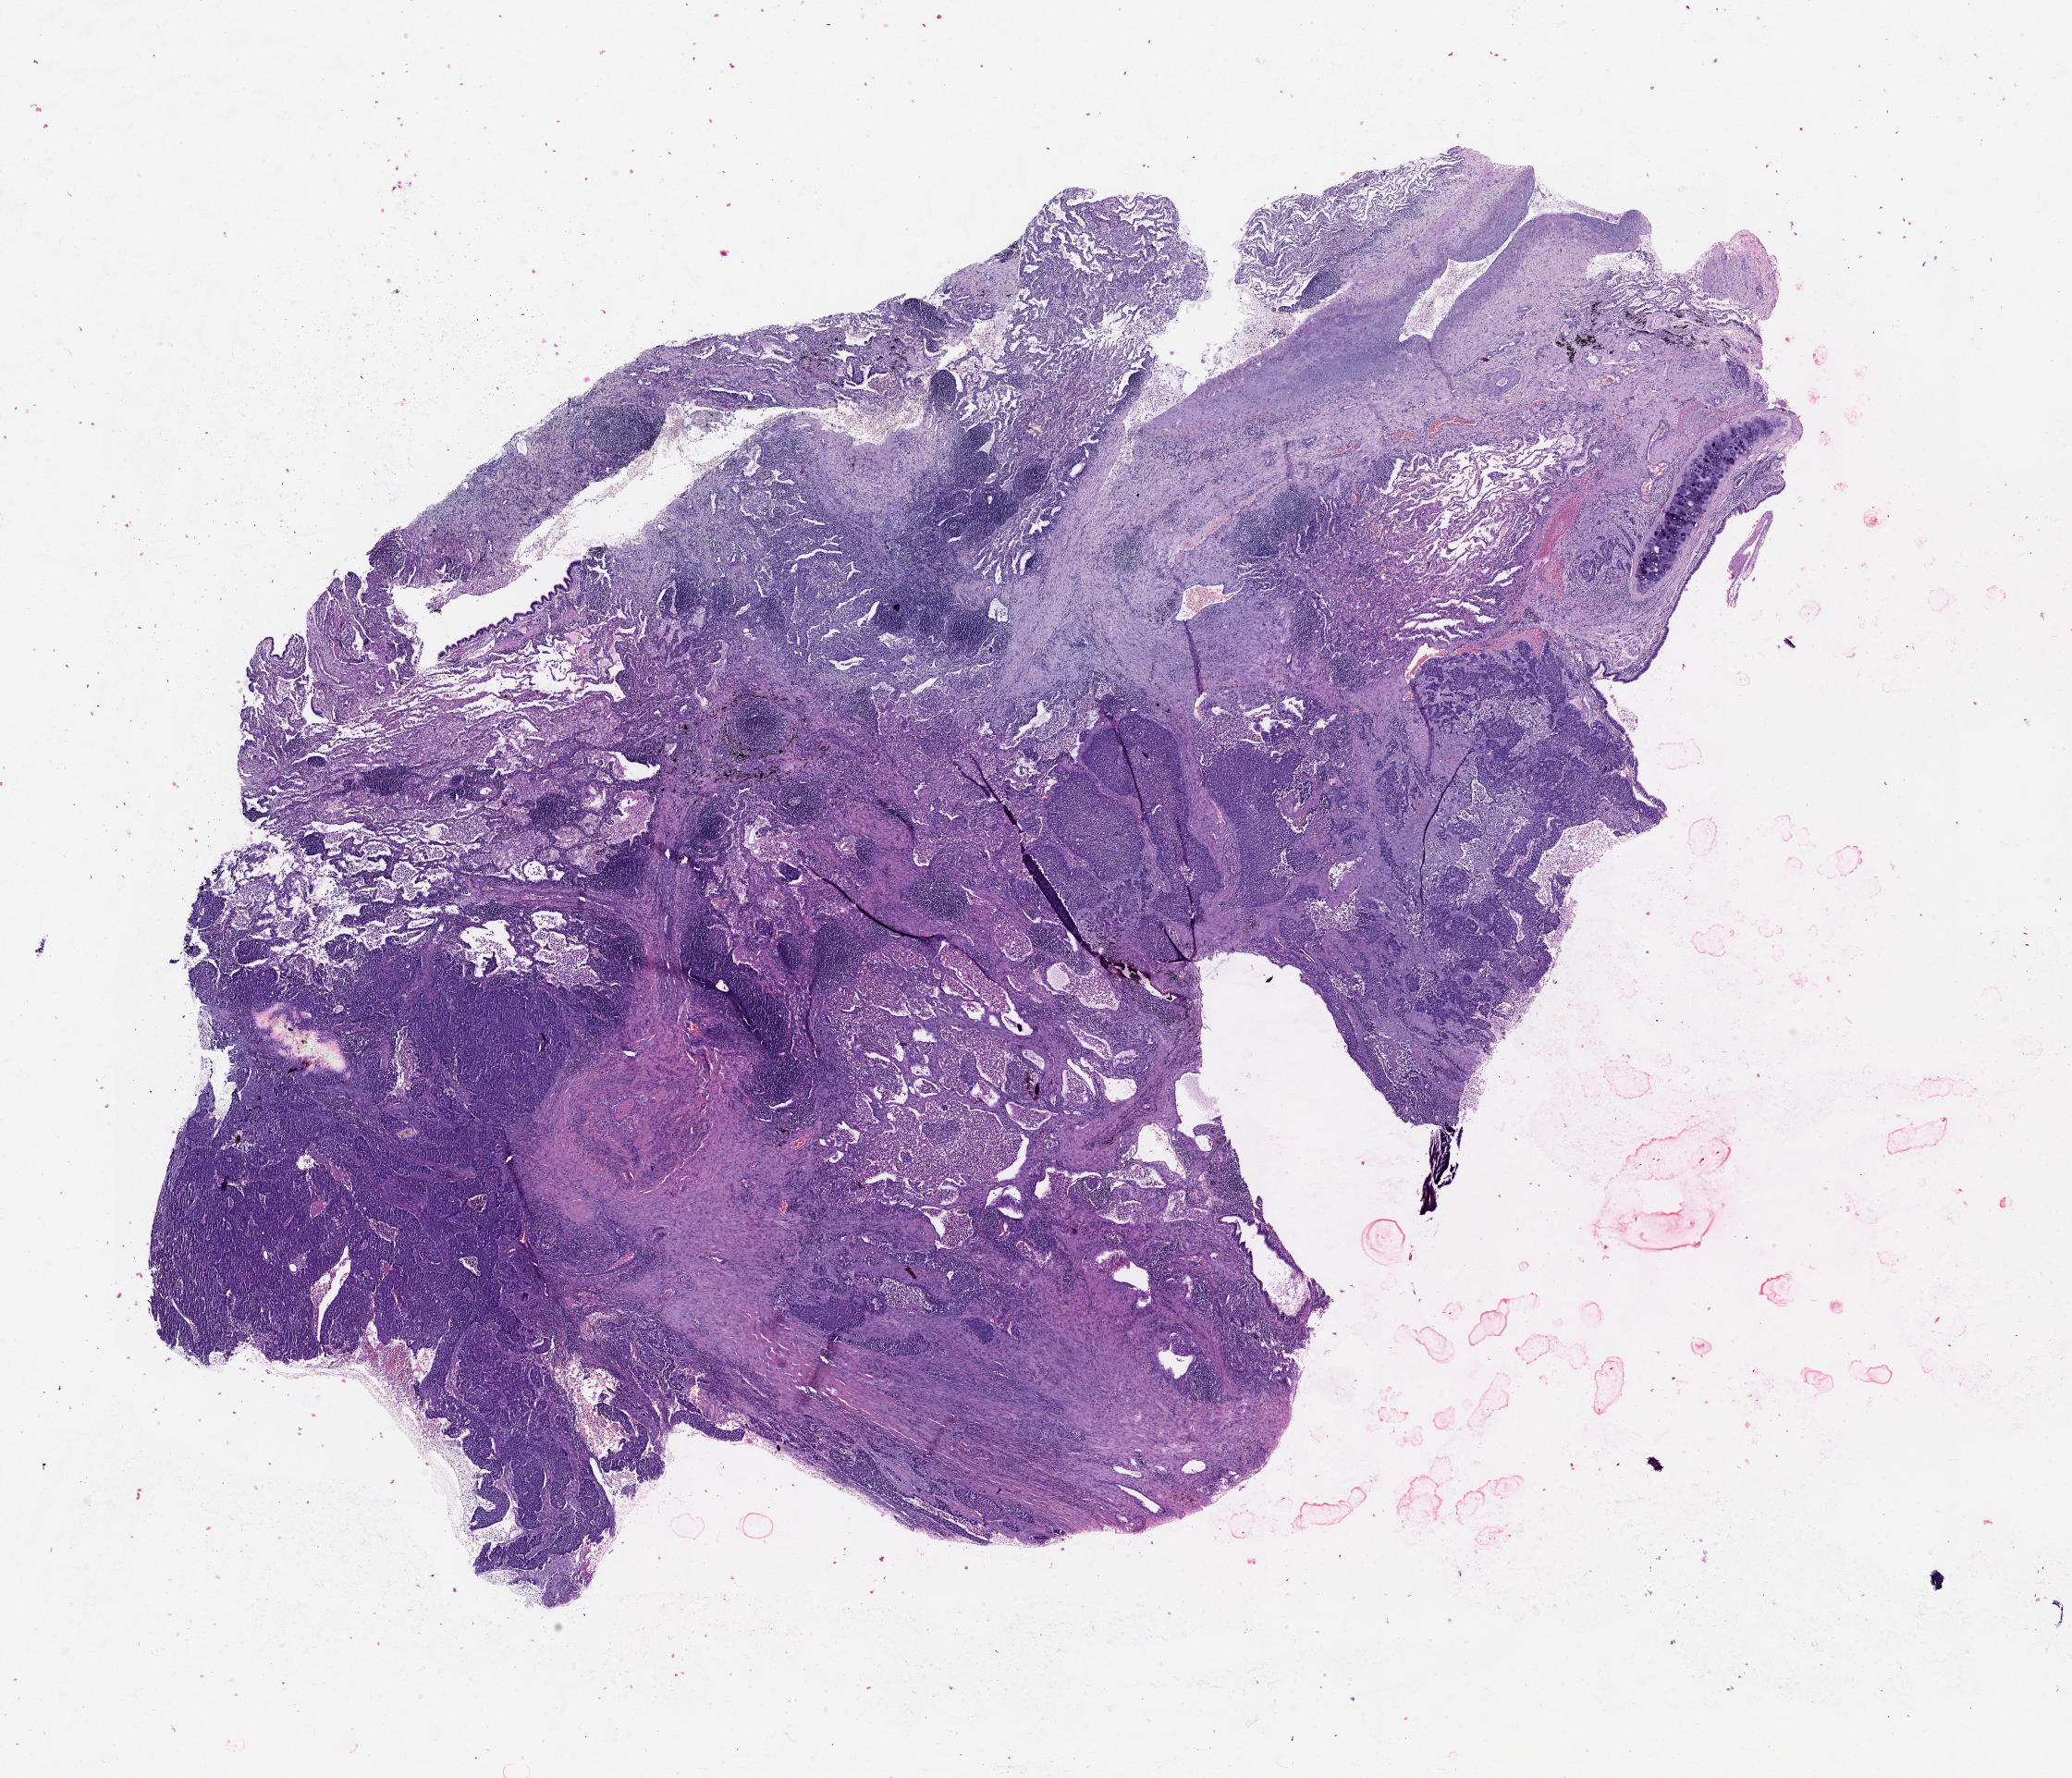
Digitized H&E-stained tissue section (whole slide) — low-resolution overview of the scanned area, about 18.0 x 15.5 mm (acquisition: 20x scan); tumour tissue sample, lung. Female, 62 y/o.
Patient diagnosis (cohort enrolment): squamous cell carcinoma (lung).